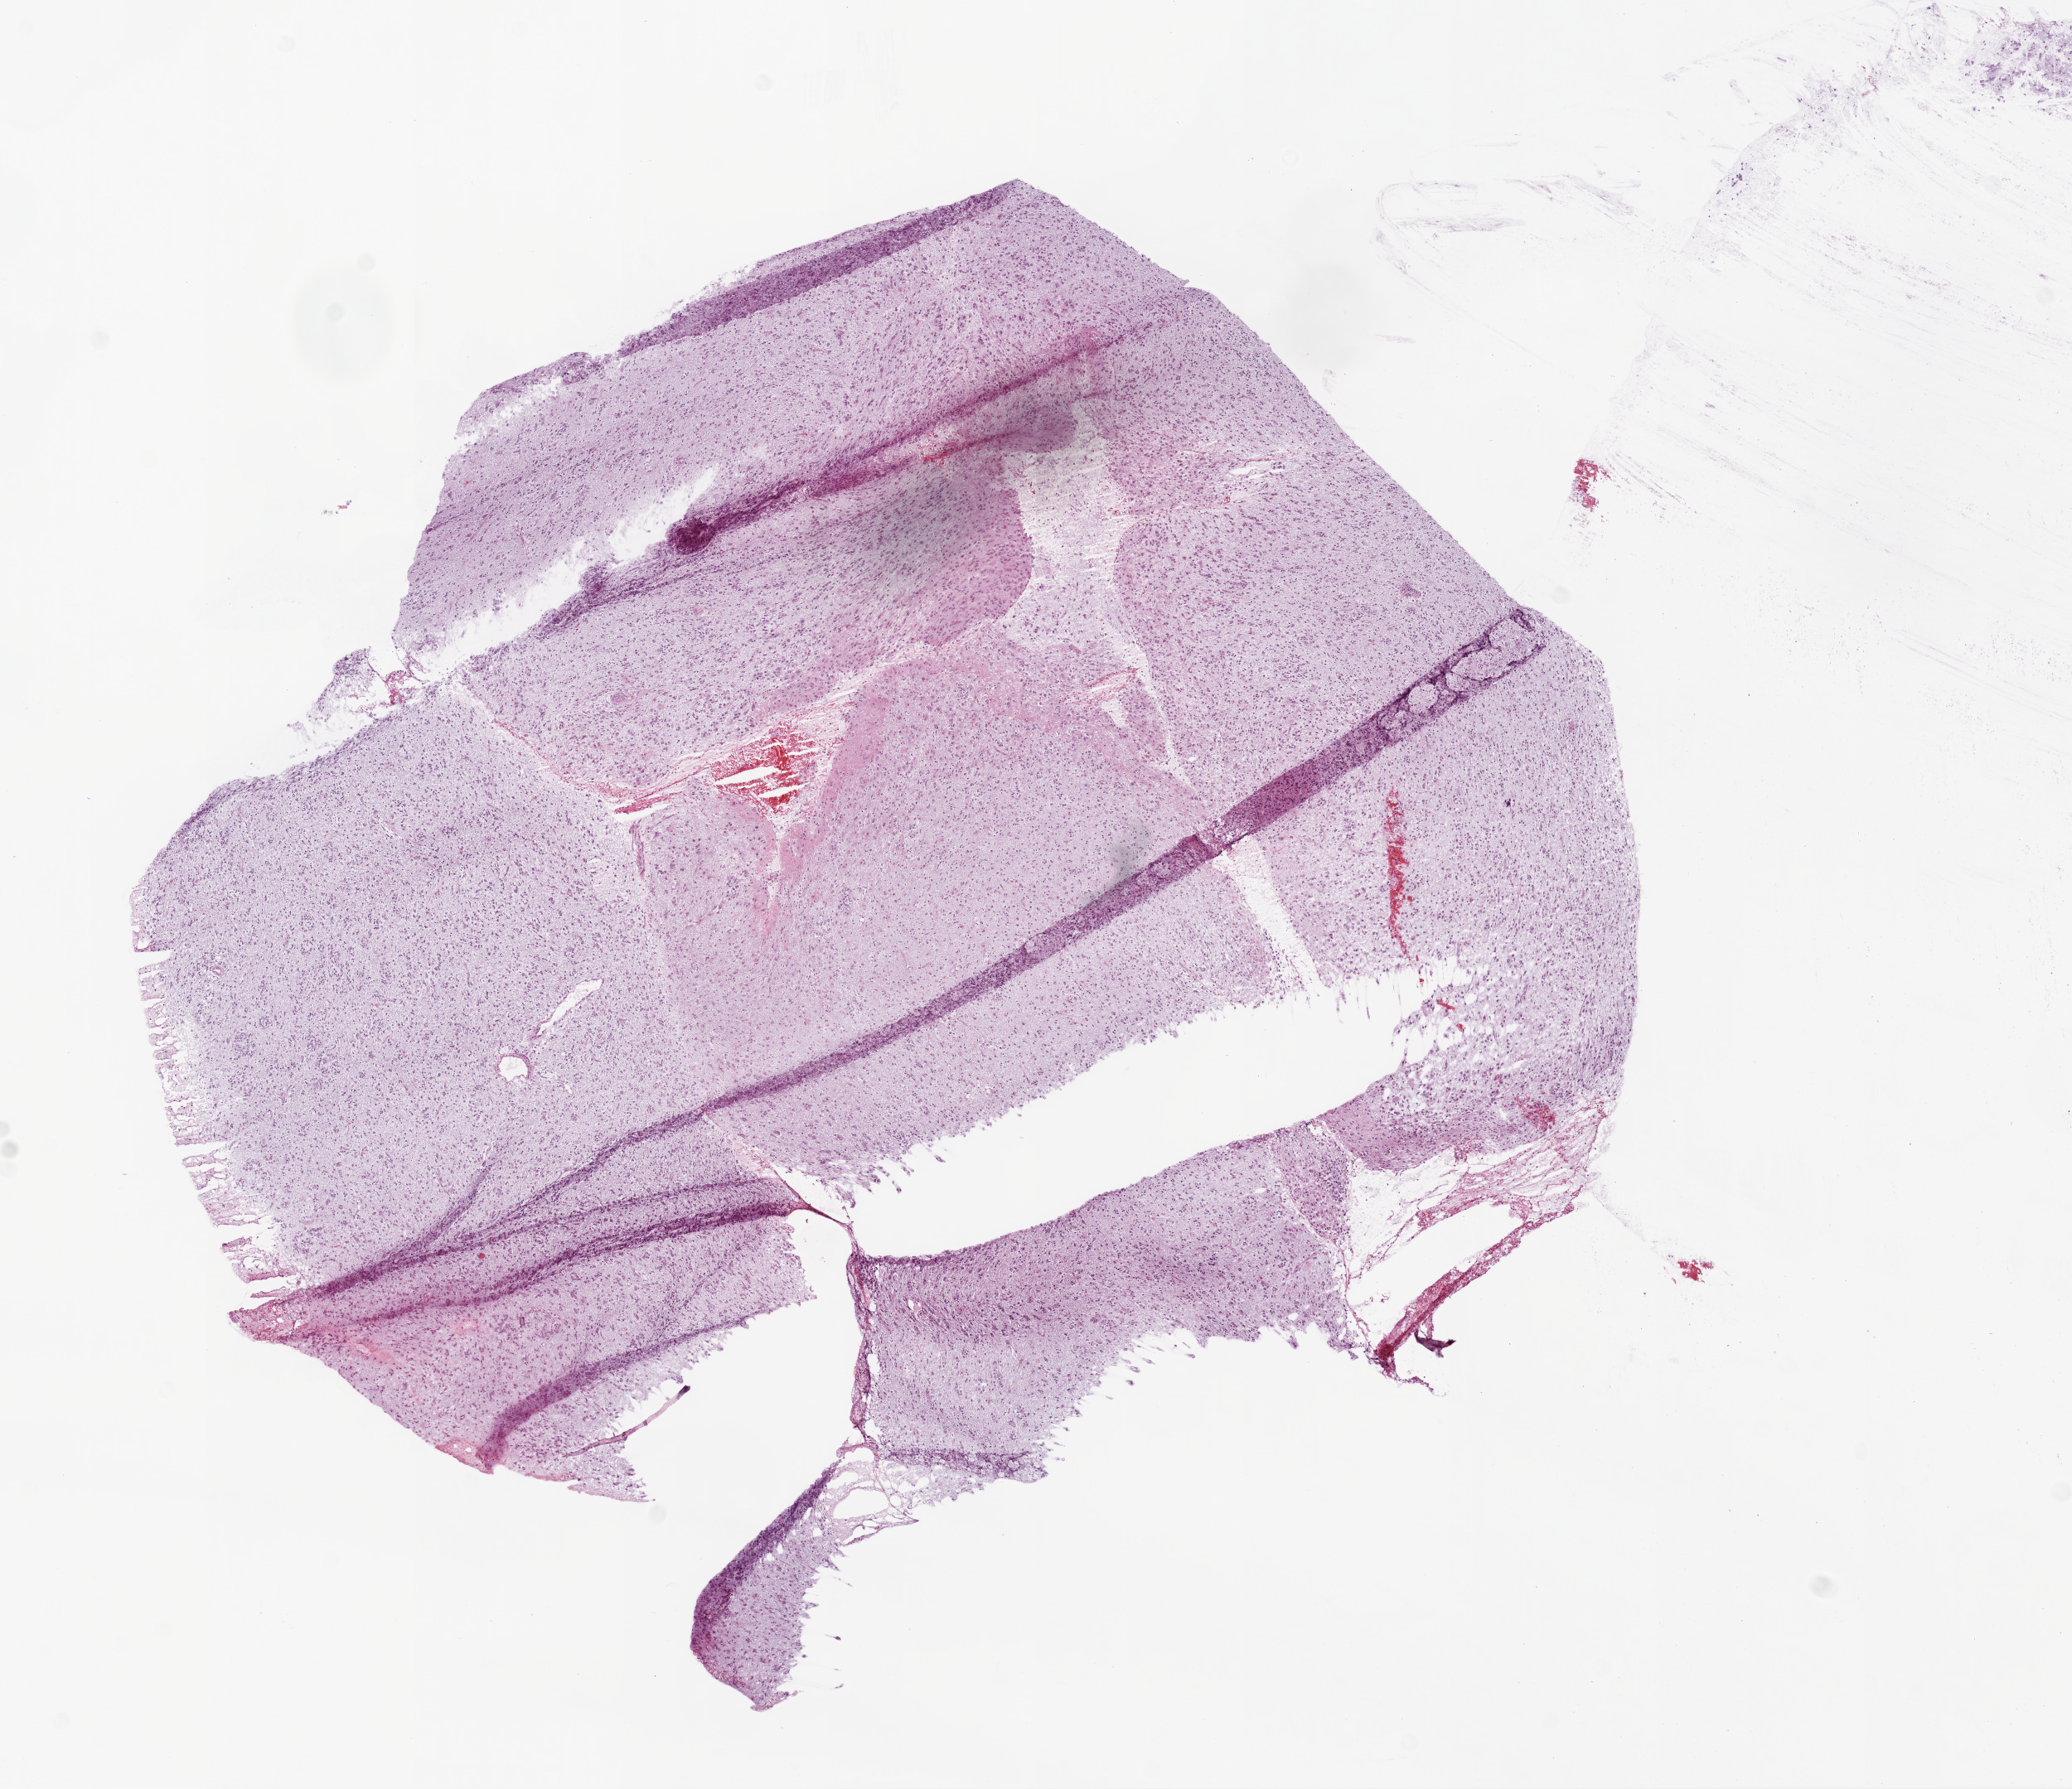
Whole-slide histology image, H&E-stained, low-resolution overview of the scanned area, about 10.0 x 8.7 mm (acquisition: 20x scan), frozen section, primary tumour sample from the brain. Female patient; age at initial diagnosis 81 years. Composition of this section per pathologist review: tumour cells 60%, tumour nuclei 60%, normal cells 30%, stromal cells 5%, necrosis 5%.
Diagnosis: Glioblastoma.